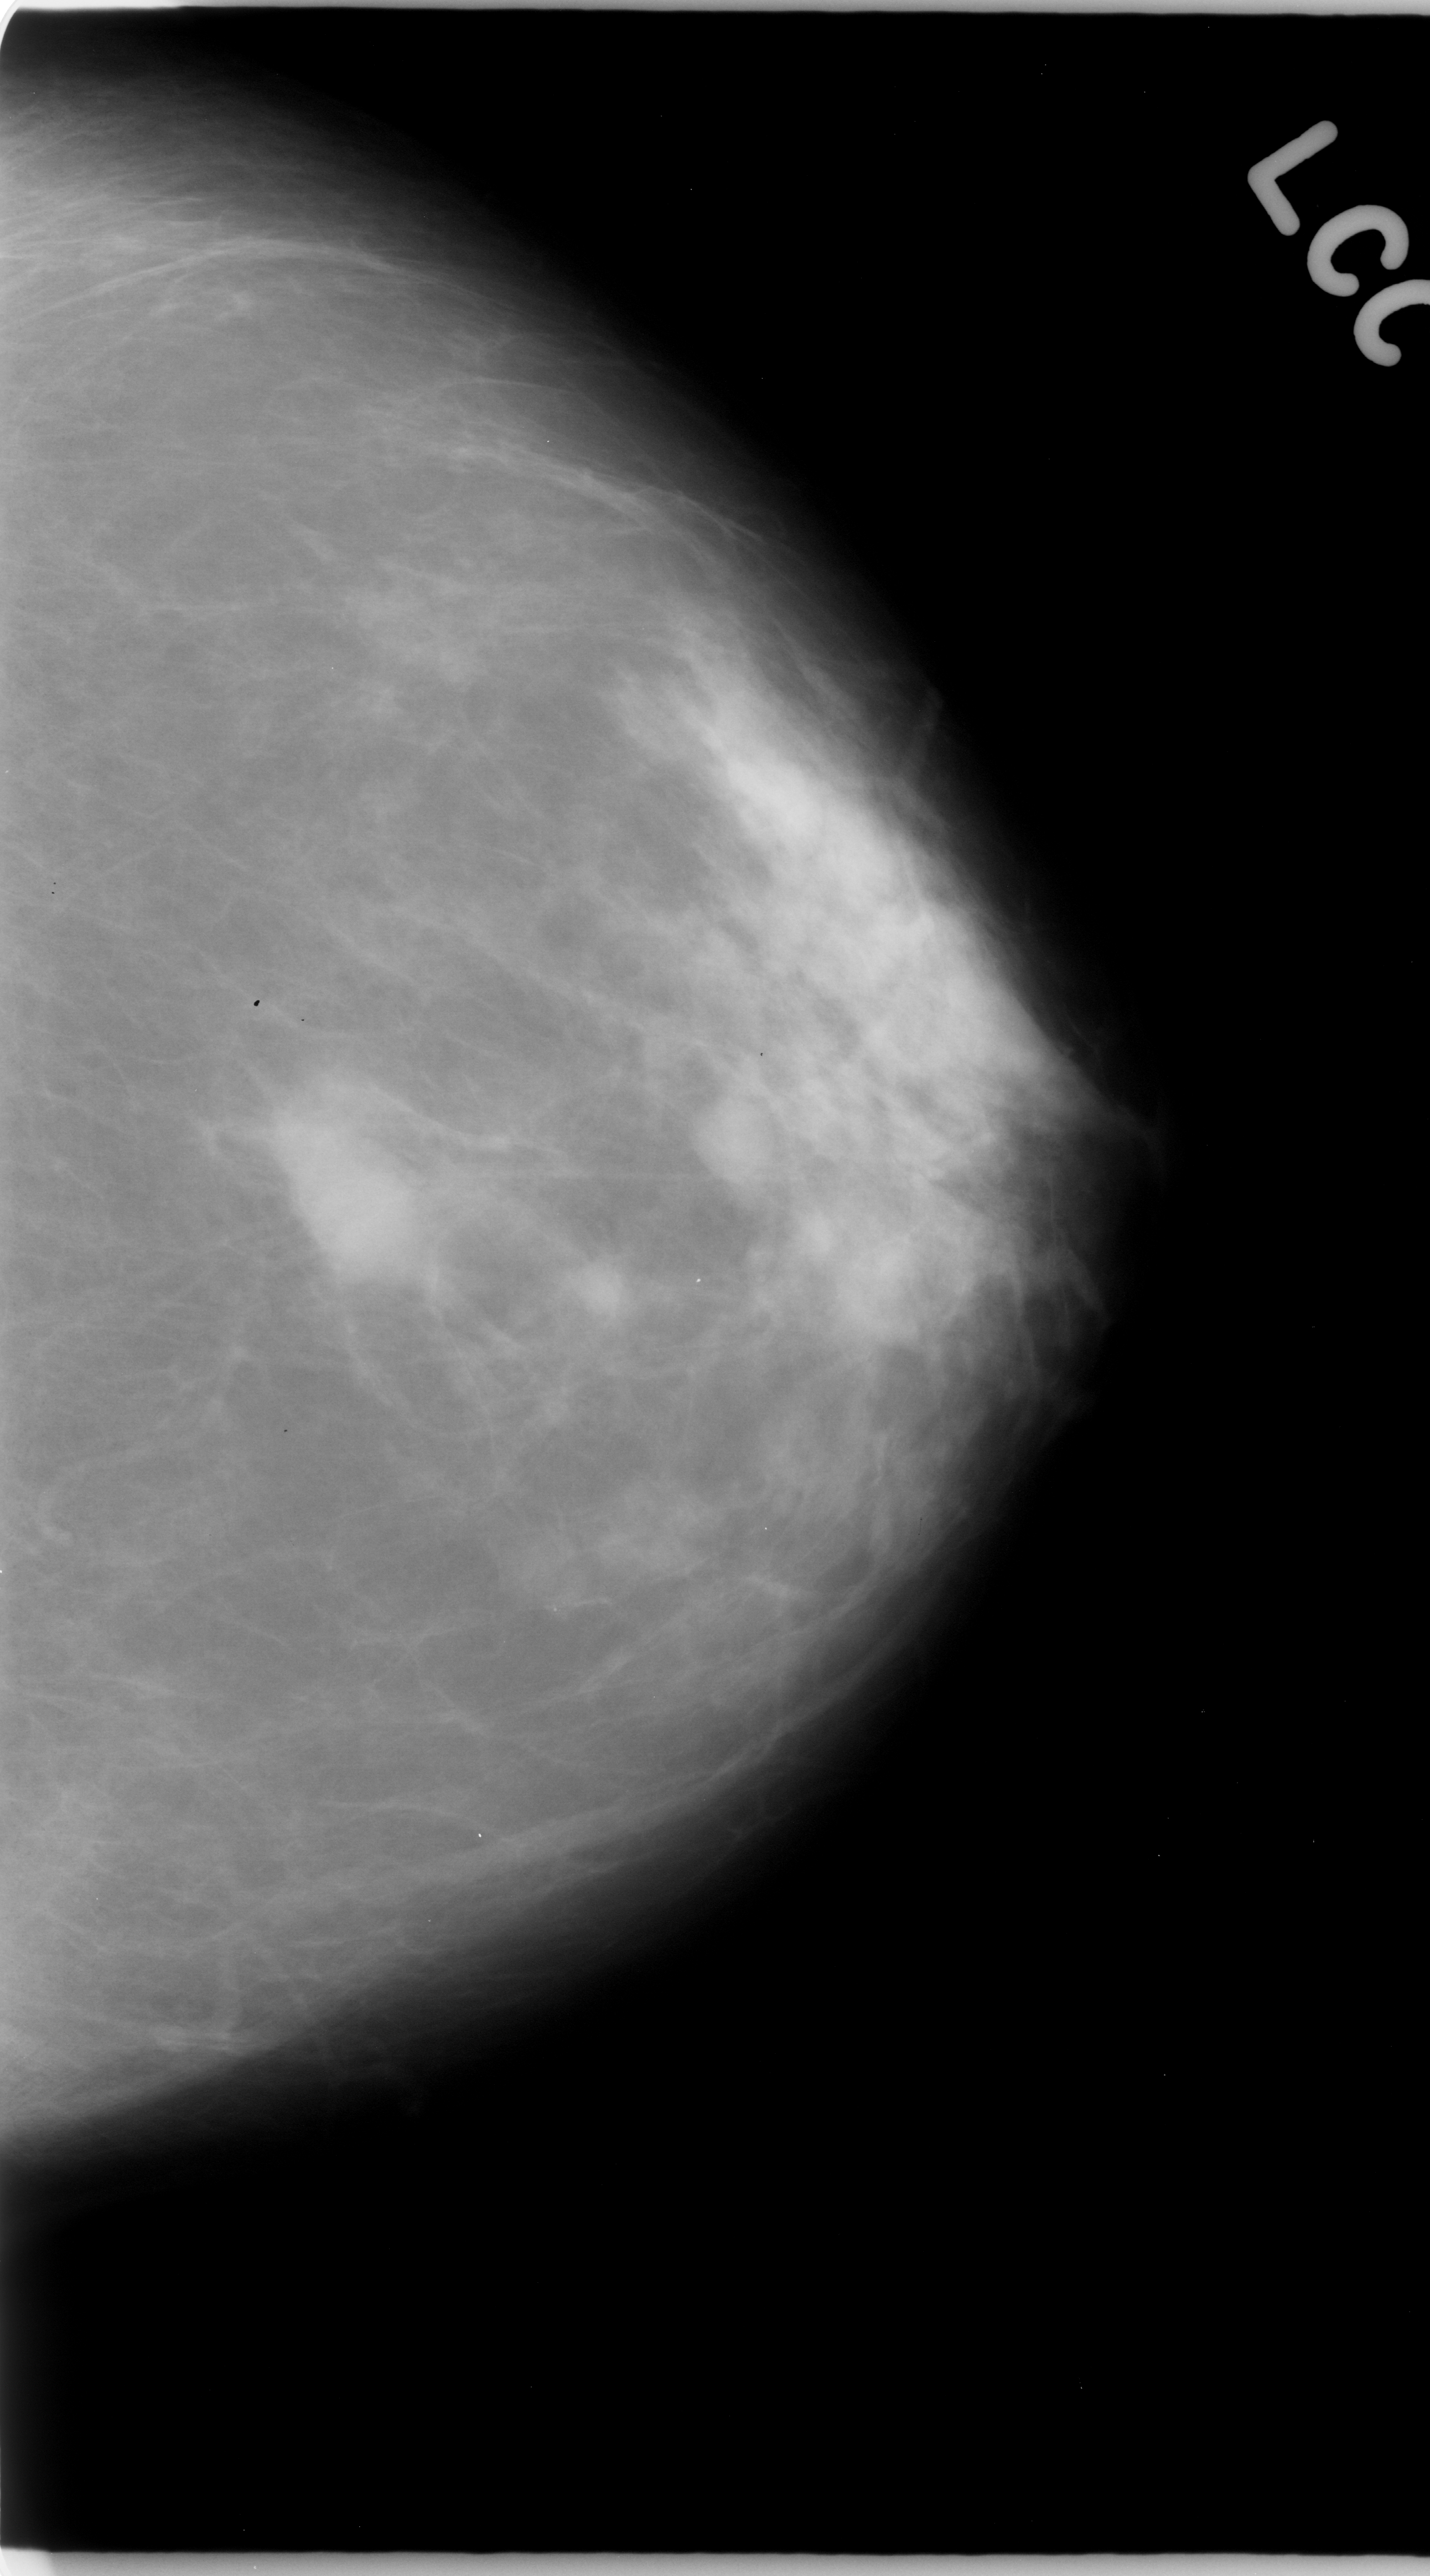
Digitized screen-film mammogram. Left breast. Craniocaudal (CC) view. BI-RADS breast density category 2 (scale 1–4). 1430 × 2576 image matrix.
Expert-marked regions of interest on this film, with their recorded descriptors:
- Finding 1 of 2: mass, margins ill defined; BI-RADS assessment category 5; pathology result (as recorded, not read from the image): malignant: bounding box <263,1115,426,1293> (left, top, right, bottom; pixels)
- Finding 2 of 2: mass, shape oval, margins circumscribed; BI-RADS assessment category 3; pathology (as recorded): benign: <679,1076,785,1212>